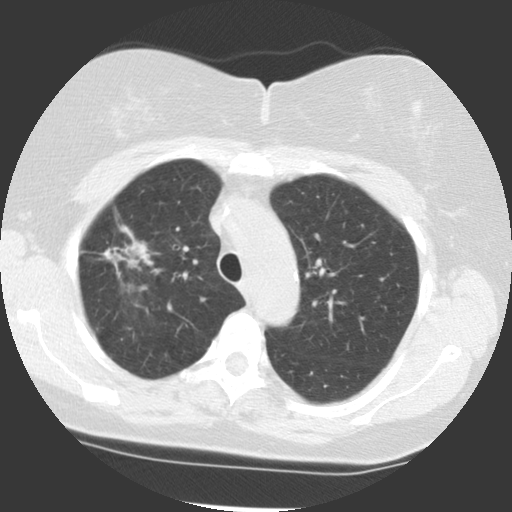
Low-dose screening chest CT, one axial slice; slice 87 of 113 in the series (ordered by position); reconstruction kernel STANDARD; lung window (W 1500 / L -600 HU); 512 × 512 image matrix, field of view 320 × 320 mm.
Structures marked on this image (manually delineated by an expert):
- lesion 1 (tumor, upper lobe of right lung): box from (x=103, y=227) to (x=153, y=276) px